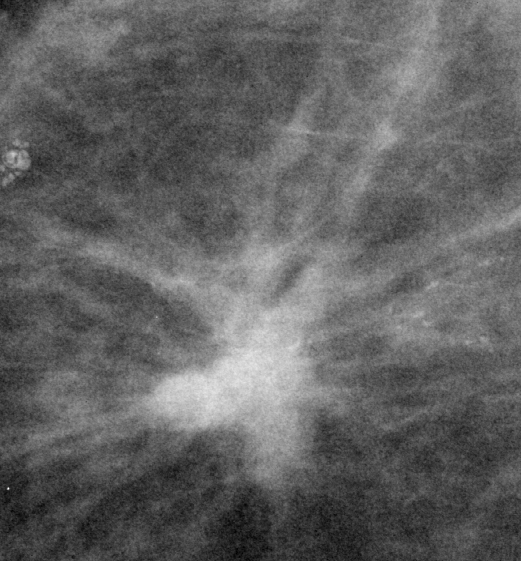
Crop from a digitized film mammogram around one marked abnormality; right breast; MLO view.
Marked abnormality: calcifications, morphology fine linear branching, distribution clustered / linear; BI-RADS assessment category 5; subtlety rating 4 on a 1 (subtle) to 5 (obvious) scale; pathology result (as recorded, not read from the image): malignant.